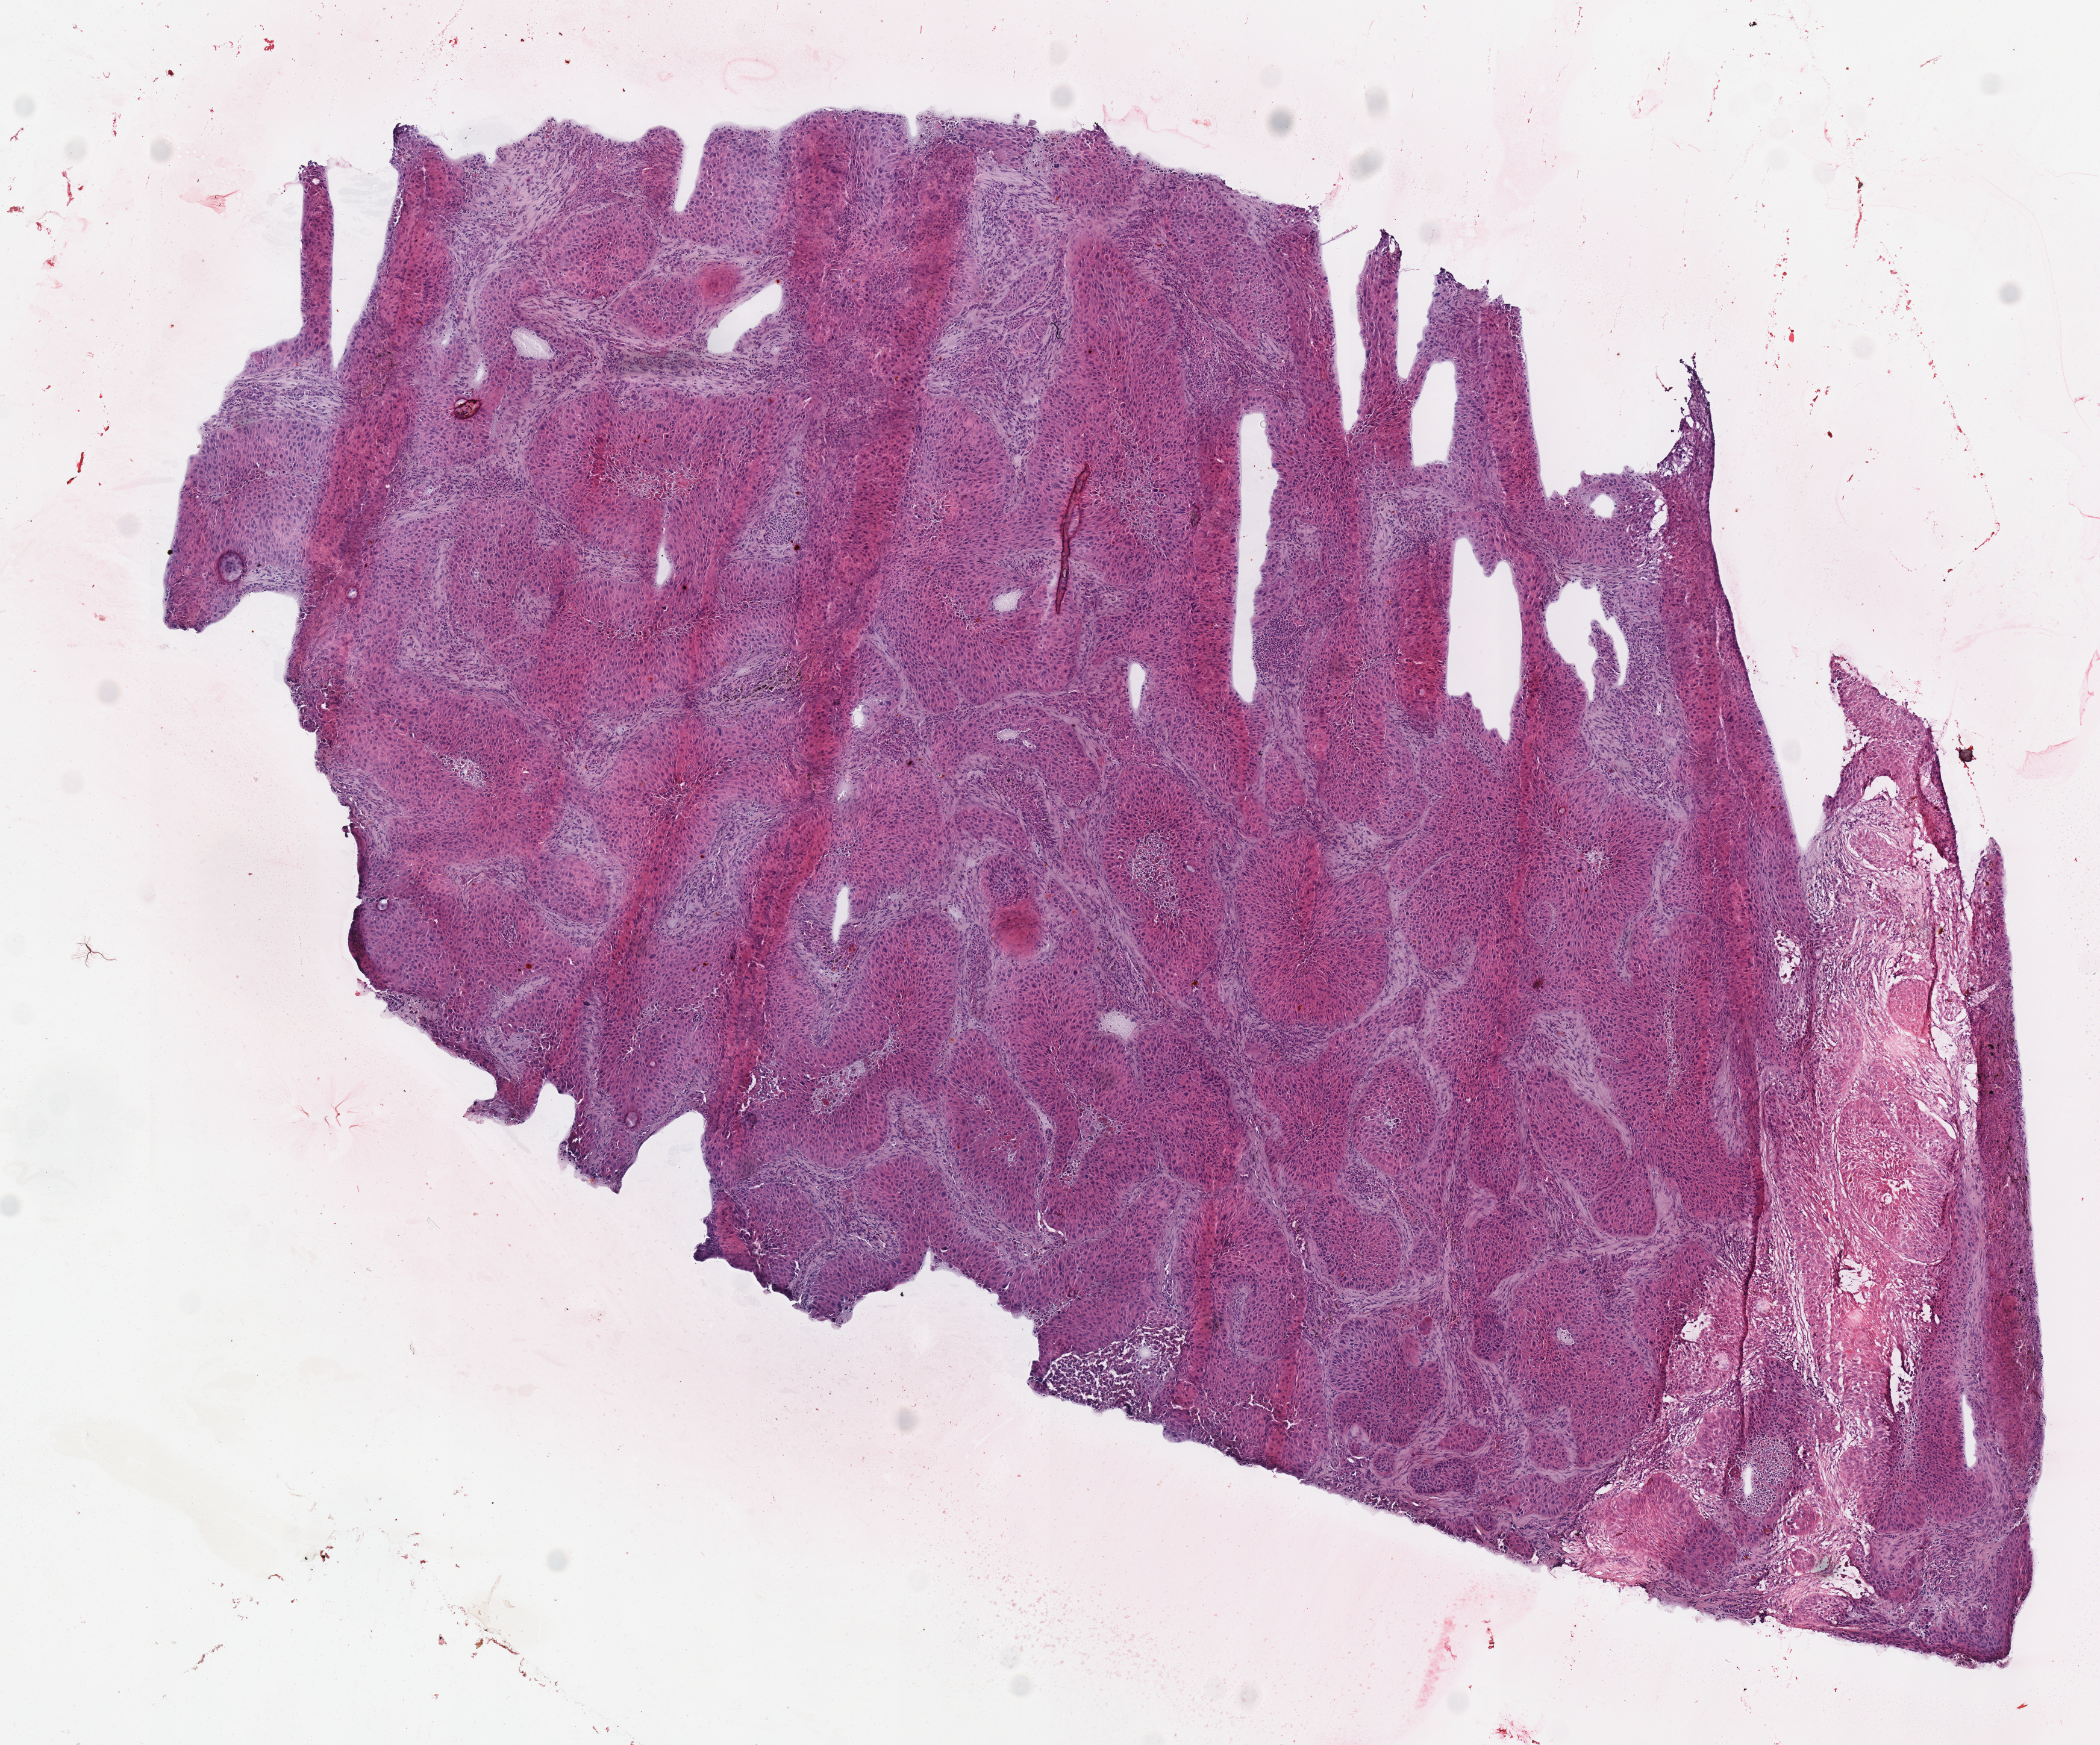
Whole-slide histology image, Hematoxylin and eosin (H&E) stained — low-resolution overview of the scanned area, about 6.9 x 5.7 mm (slide scanned at 40x); frozen section from the top of the tissue portion; primary tumour sample from the lung. Female, age 57 years at initial diagnosis. Pathologist review of this section (percent, as recorded): tumour cells 92%, tumour nuclei 85%, normal cells 0%, stromal cells 5%, necrosis 3%. Infiltration values recorded for this section: lymphocyte infiltration 10%.
Histologic diagnosis: Squamous cell carcinoma, NOS. AJCC pathologic stage: IIIA.